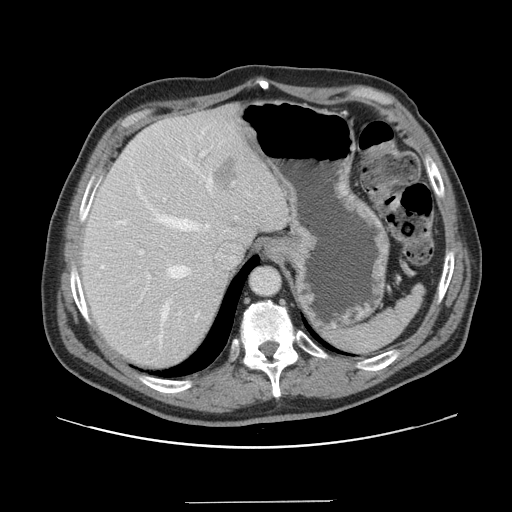
Contrast-enhanced abdominal CT, one axial slice; position 119 of 151 along the scan axis; intravenous contrast given; soft-tissue window (W 400 / L 40 HU); 2.5 mm slice thickness; 512 × 512 image matrix. Male patient, age 63 years. From the clinical record (not read from this slice): diagnosis: colorectal cancer liver metastases, imaged before liver resection; multiple liver metastases: no; largest metastasis: 2.1 cm; chemotherapy before resection: no.
Structures marked on this image (outlined manually by an expert reader):
- hepatic veins: bounding box [x1, y1, x2, y2] px = [102, 177, 212, 321]
- liver: [80, 107, 289, 369]
- planned liver remnant (the part of the liver to remain after resection): [80, 117, 257, 369]
- portal vein (with intrahepatic branches): [139, 152, 205, 279]
- liver metastasis: [214, 157, 235, 185]